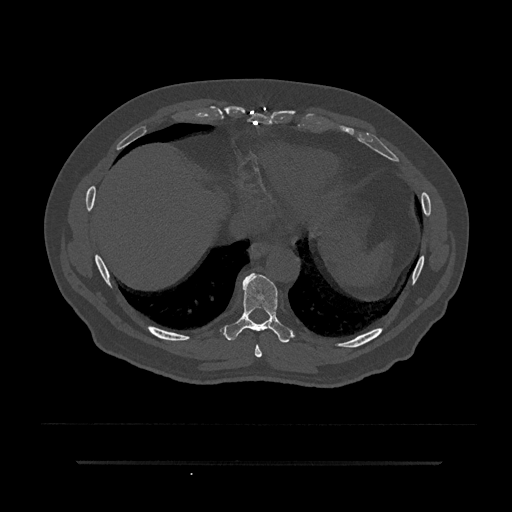
CT including the spine, one axial slice; slice 383 of 797 in the series (ordered by position); reconstruction kernel Br40s/3; 120 kVp; bone window (W 1800 / L 400 HU); 0.5 mm slice thickness; 512 × 512 image matrix, field of view 464 × 464 mm. Patient: male, 59 years. From the clinical record (not read from this slice): primary cancer: bile ducts.
Structures marked on this image (semi-automatic segmentation, software-assisted and operator-edited):
- T8 vertebra: bounding box (x1, y1, x2, y2) in pixels: (255, 344, 262, 358)
- T9 vertebra: (223, 273, 293, 343)